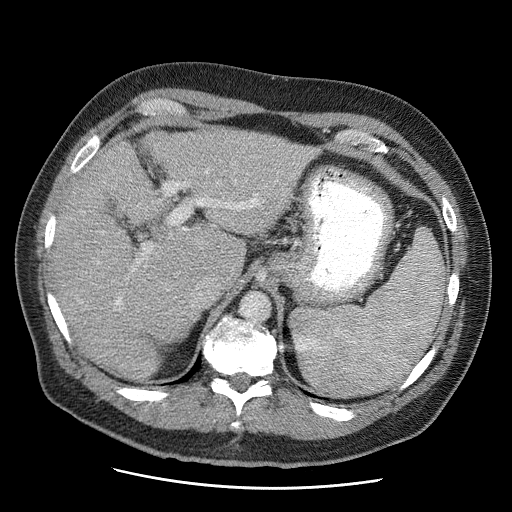
Contrast-enhanced abdominal CT (liver protocol), one axial slice. Slice 37 of 81 in the series (ordered by position). Soft-tissue window (W 400 / L 40 HU). 2.5 mm slice thickness. 512 × 512 image matrix, field of view 380 × 380 mm. From the clinical record (not read from this slice): diagnosis: hepatocellular carcinoma (patient treated with transarterial chemoembolisation; whether this scan precedes or follows treatment is not stated here); TNM stage (as recorded): Stage-IIIA; Child-Pugh class: A; tumour differentiation: moderately differentiated; tumour size: 5.5 cm.
Annotated regions visible in this slice (semi-automatic segmentation, software-assisted and operator-edited):
- liver parenchyma outside the tumour (the mass and vessels are separate outlines, so this box may not span the whole liver): bounding box (x1, y1, x2, y2) in pixels: (50, 128, 317, 380)
- liver vessels: (115, 171, 258, 305)